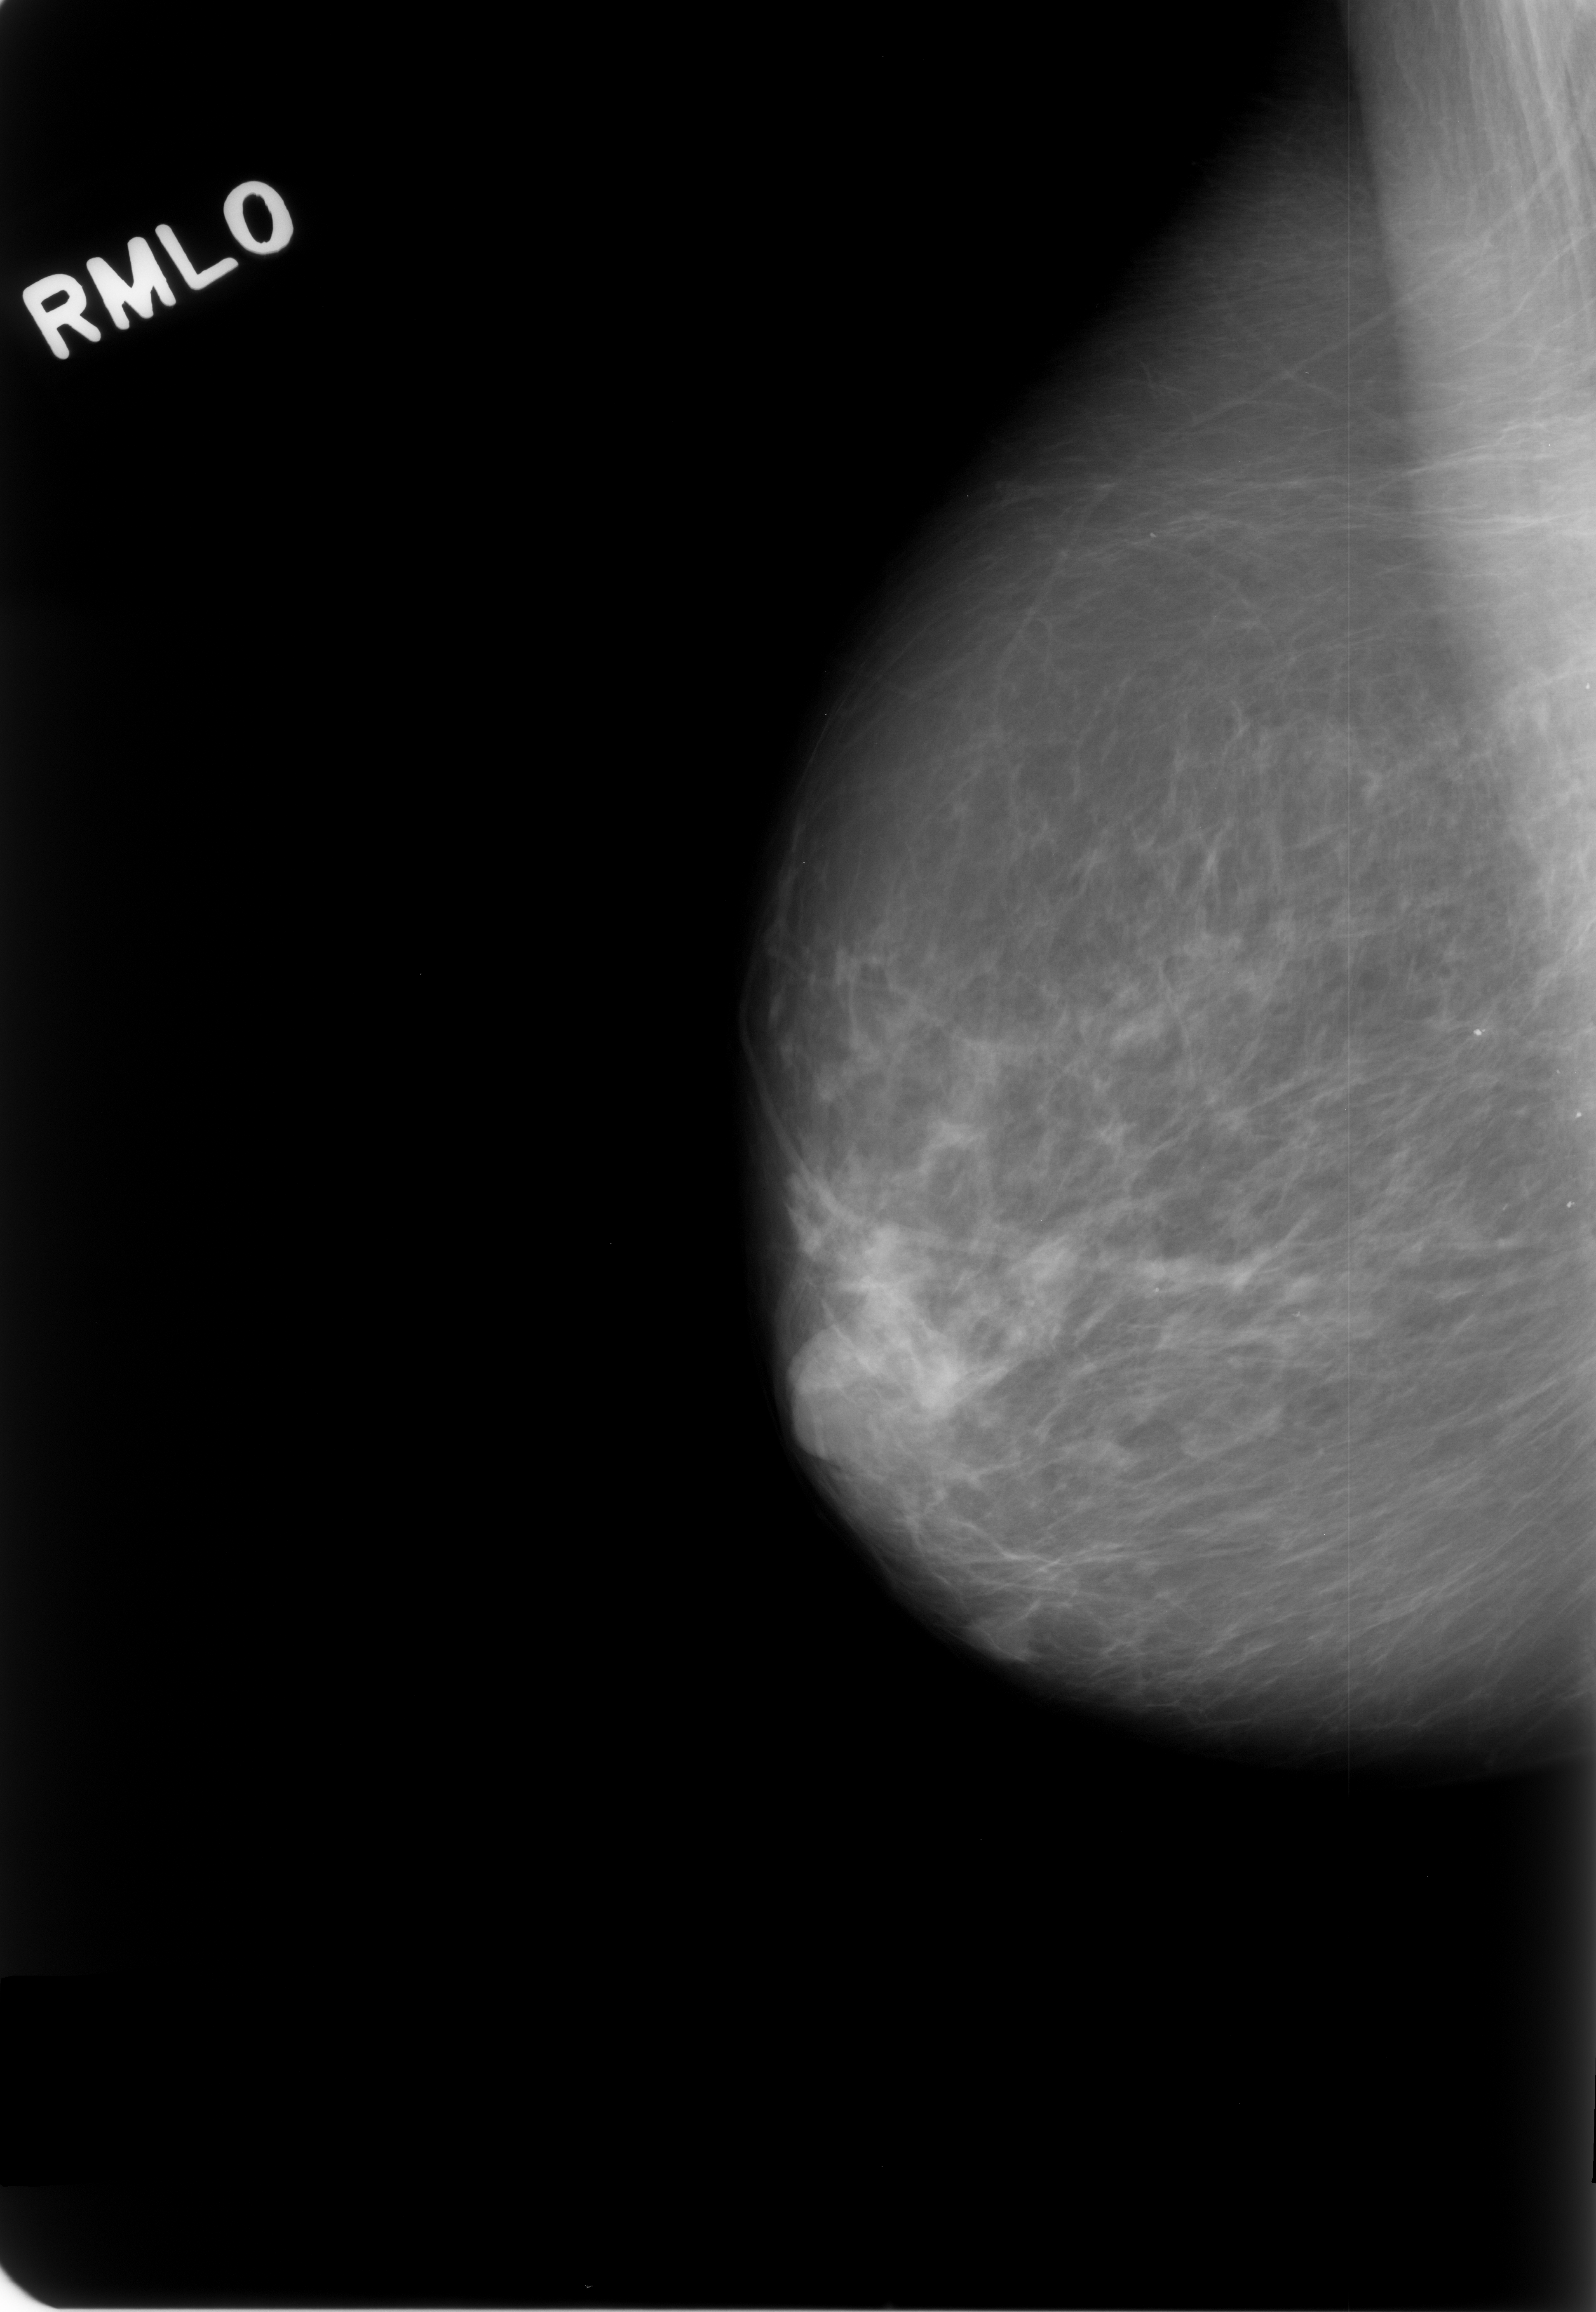
Scanned film-screen mammogram, right breast, MLO view.
Radiologist-marked abnormalities on this image: mass, shape oval, margins circumscribed; BI-RADS assessment category 3; subtlety rating 5 on a 1 (subtle) to 5 (obvious) scale; benign; no additional work-up was recommended (benign without callback).